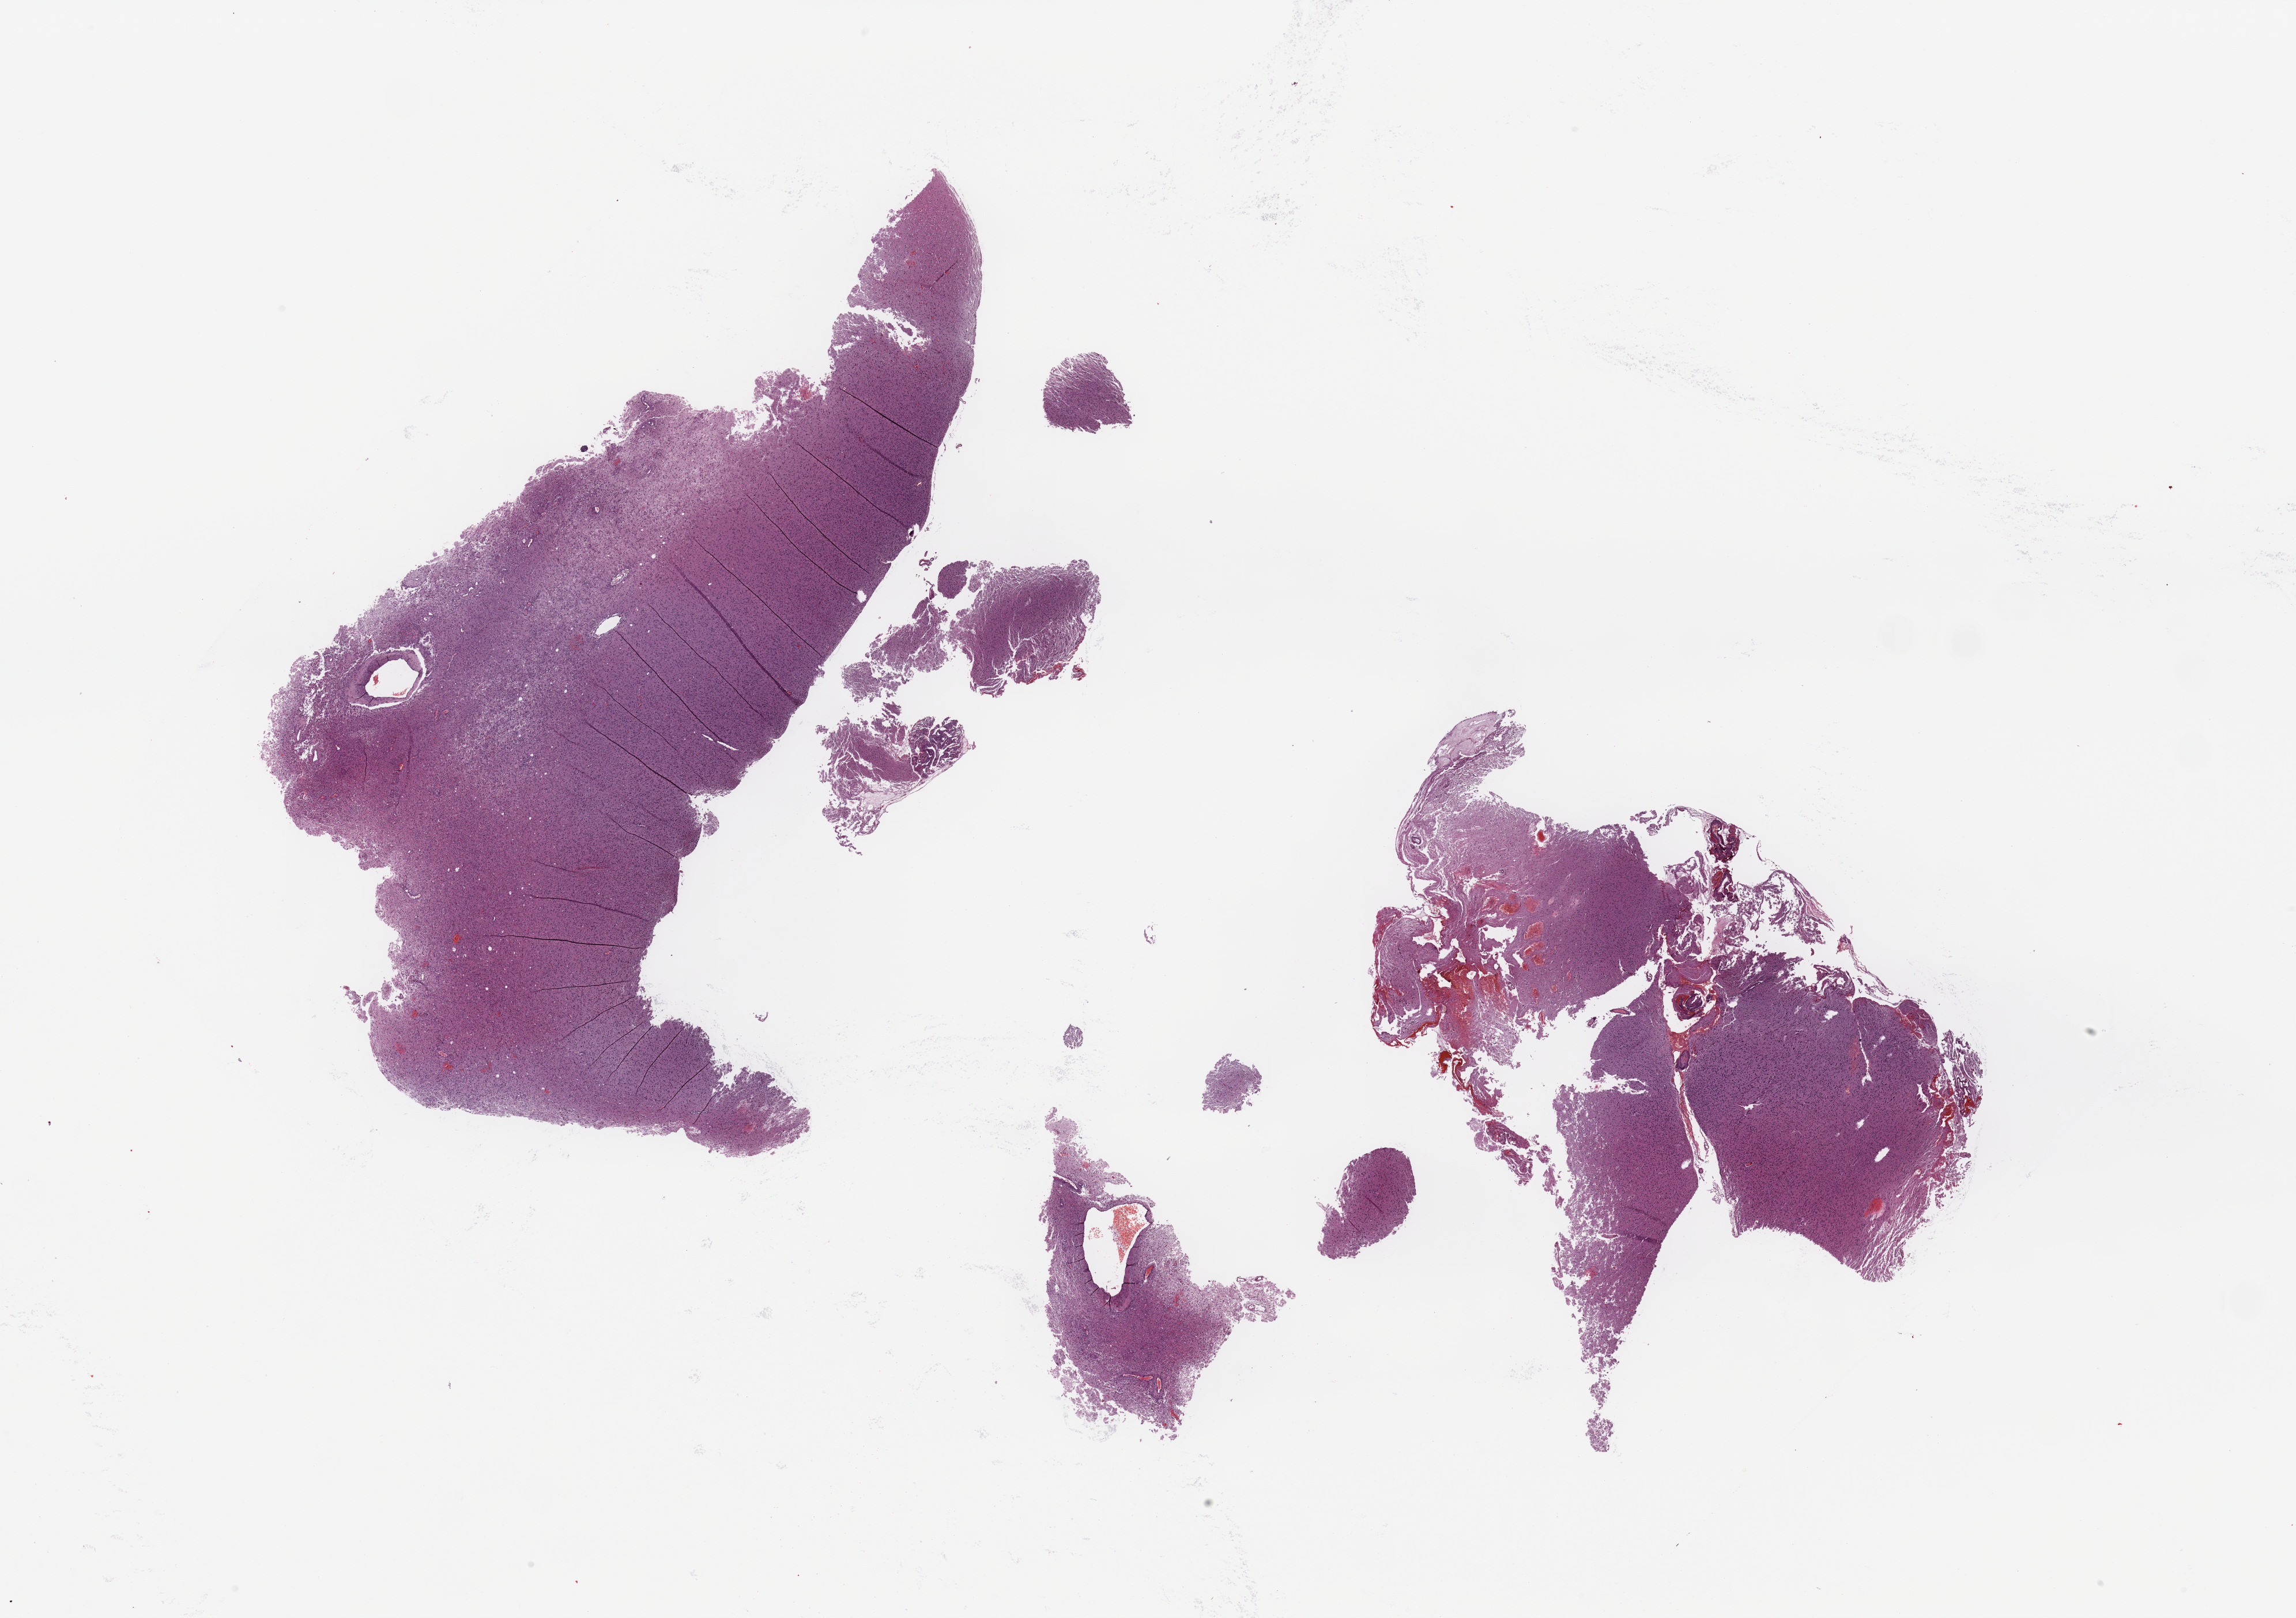
Digitized H&E-stained tissue section (whole slide), low-resolution overview of the scanned area, about 31.5 x 22.2 mm (slide scanned at 20x), tumour tissue sample, sampled site: brain. Male, 53 y/o. Slide review estimates, as recorded: tumour nuclei 75%, necrosis 5%.
Primary tumour site (as recorded): frontal lobe. Histologic diagnosis: Glioblastoma.